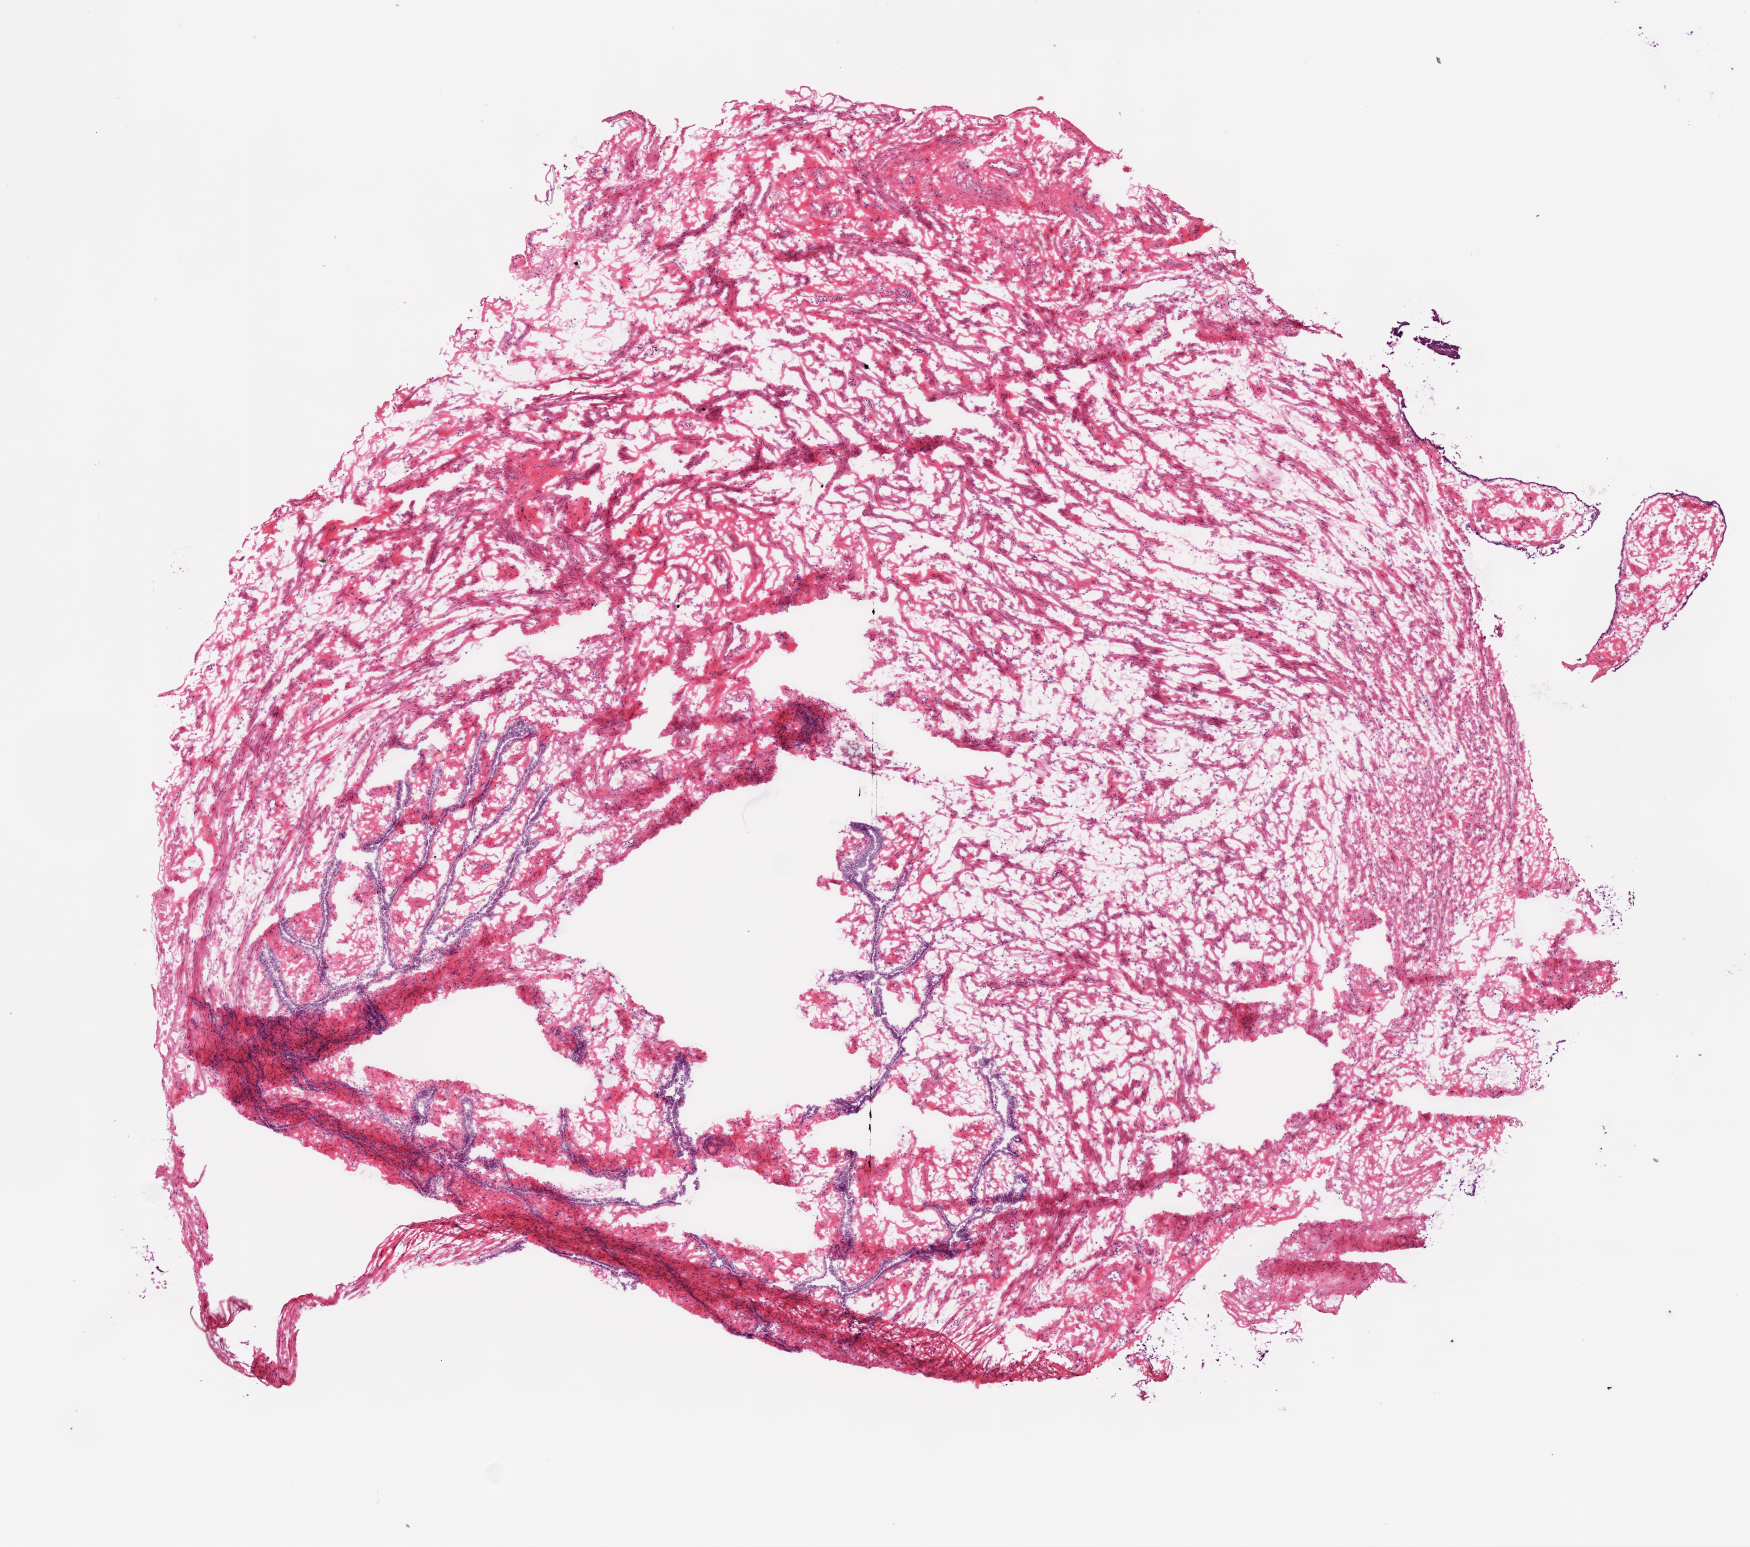
H&E whole-slide image — low-resolution overview of the scanned area, about 7.0 x 6.2 mm. Frozen section from the bottom of the tissue portion. Solid tissue normal (non-tumour tissue) sample from the ovary. Patient: female, age at initial diagnosis 73 years.
- this section: solid tissue normal (non-tumour) sample from the same patient
- patient diagnosis: Serous cystadenocarcinoma, NOS